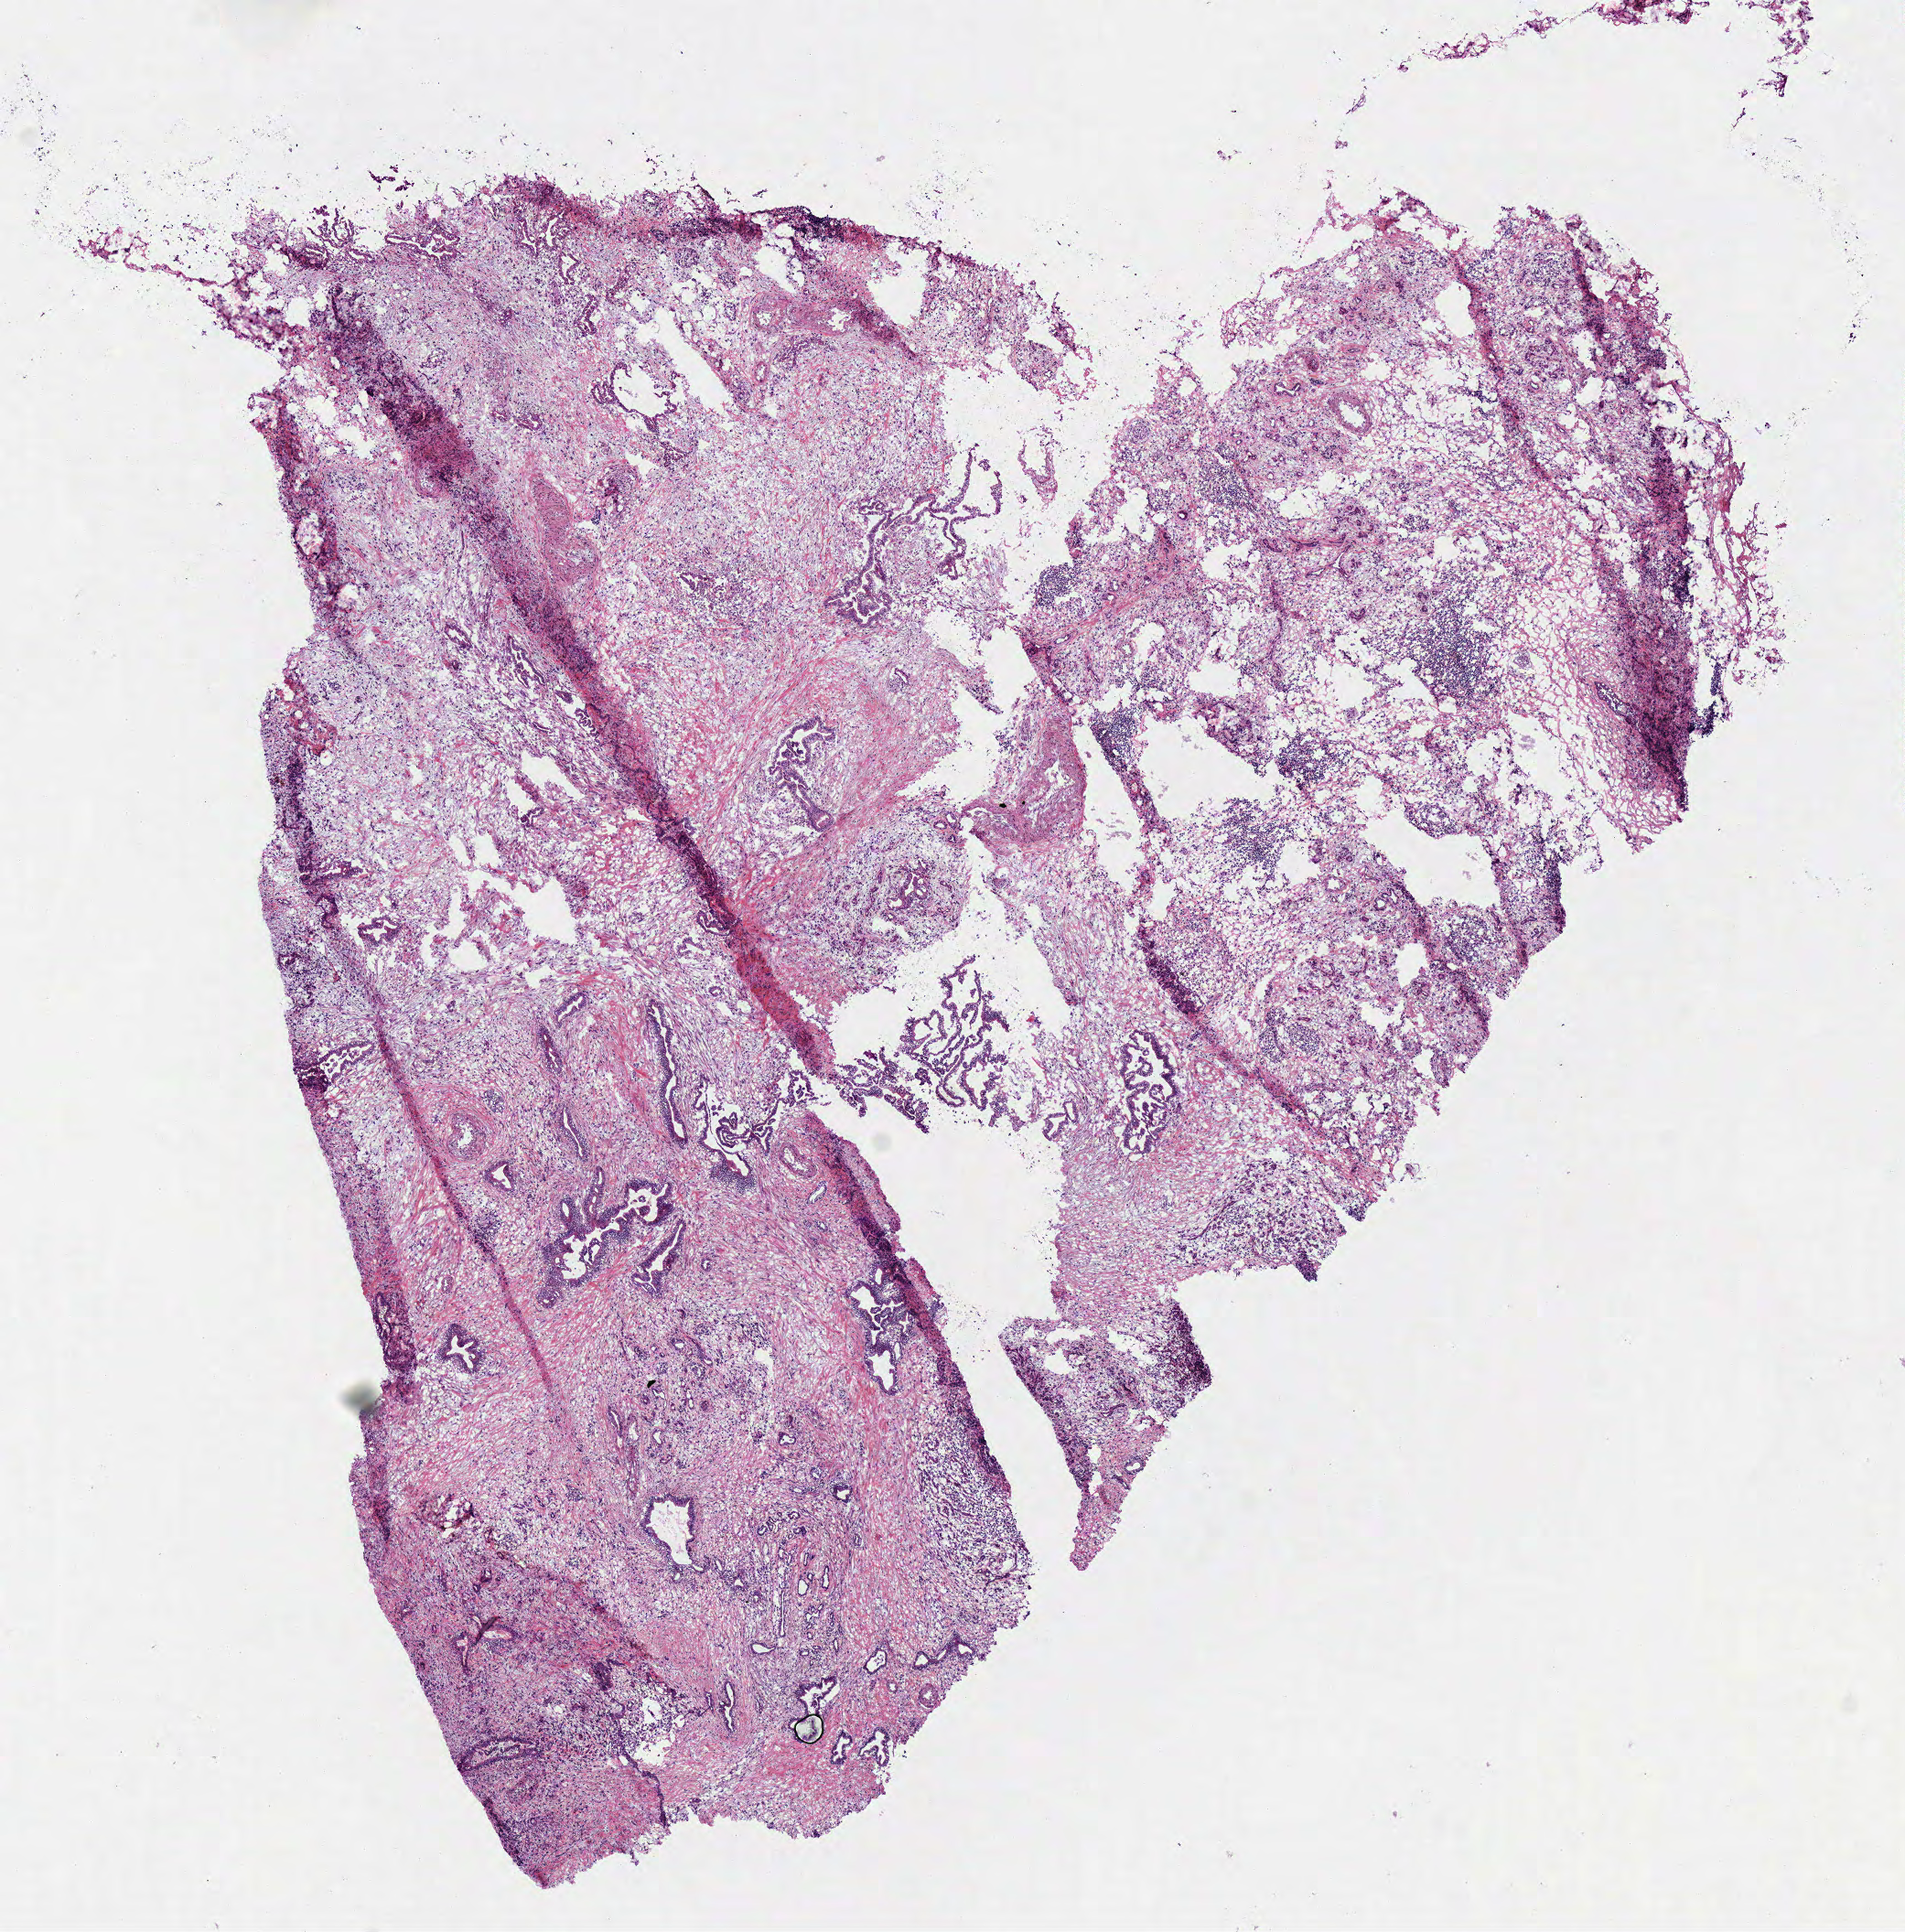
Digitized H&E-stained tissue section (whole slide) — whole scanned area (about 8.2 x 8.3 mm, acquisition: 40x scan) shown as a low-resolution overview; frozen section from the top of the tissue portion; pancreas, primary tumour sample. Male patient; age at initial diagnosis 81 years. Histologic grade: G2 (moderately differentiated). Slide review estimates, as recorded: tumour cells 50%, tumour nuclei 70%, normal cells 0%, stromal cells 50%, necrosis 0%.
AJCC pathologic stage: IIA (6th edition). Lymph nodes positive (case pathology): 0 of 5 examined. Pathologic diagnosis: Infiltrating duct carcinoma, NOS (head of pancreas).